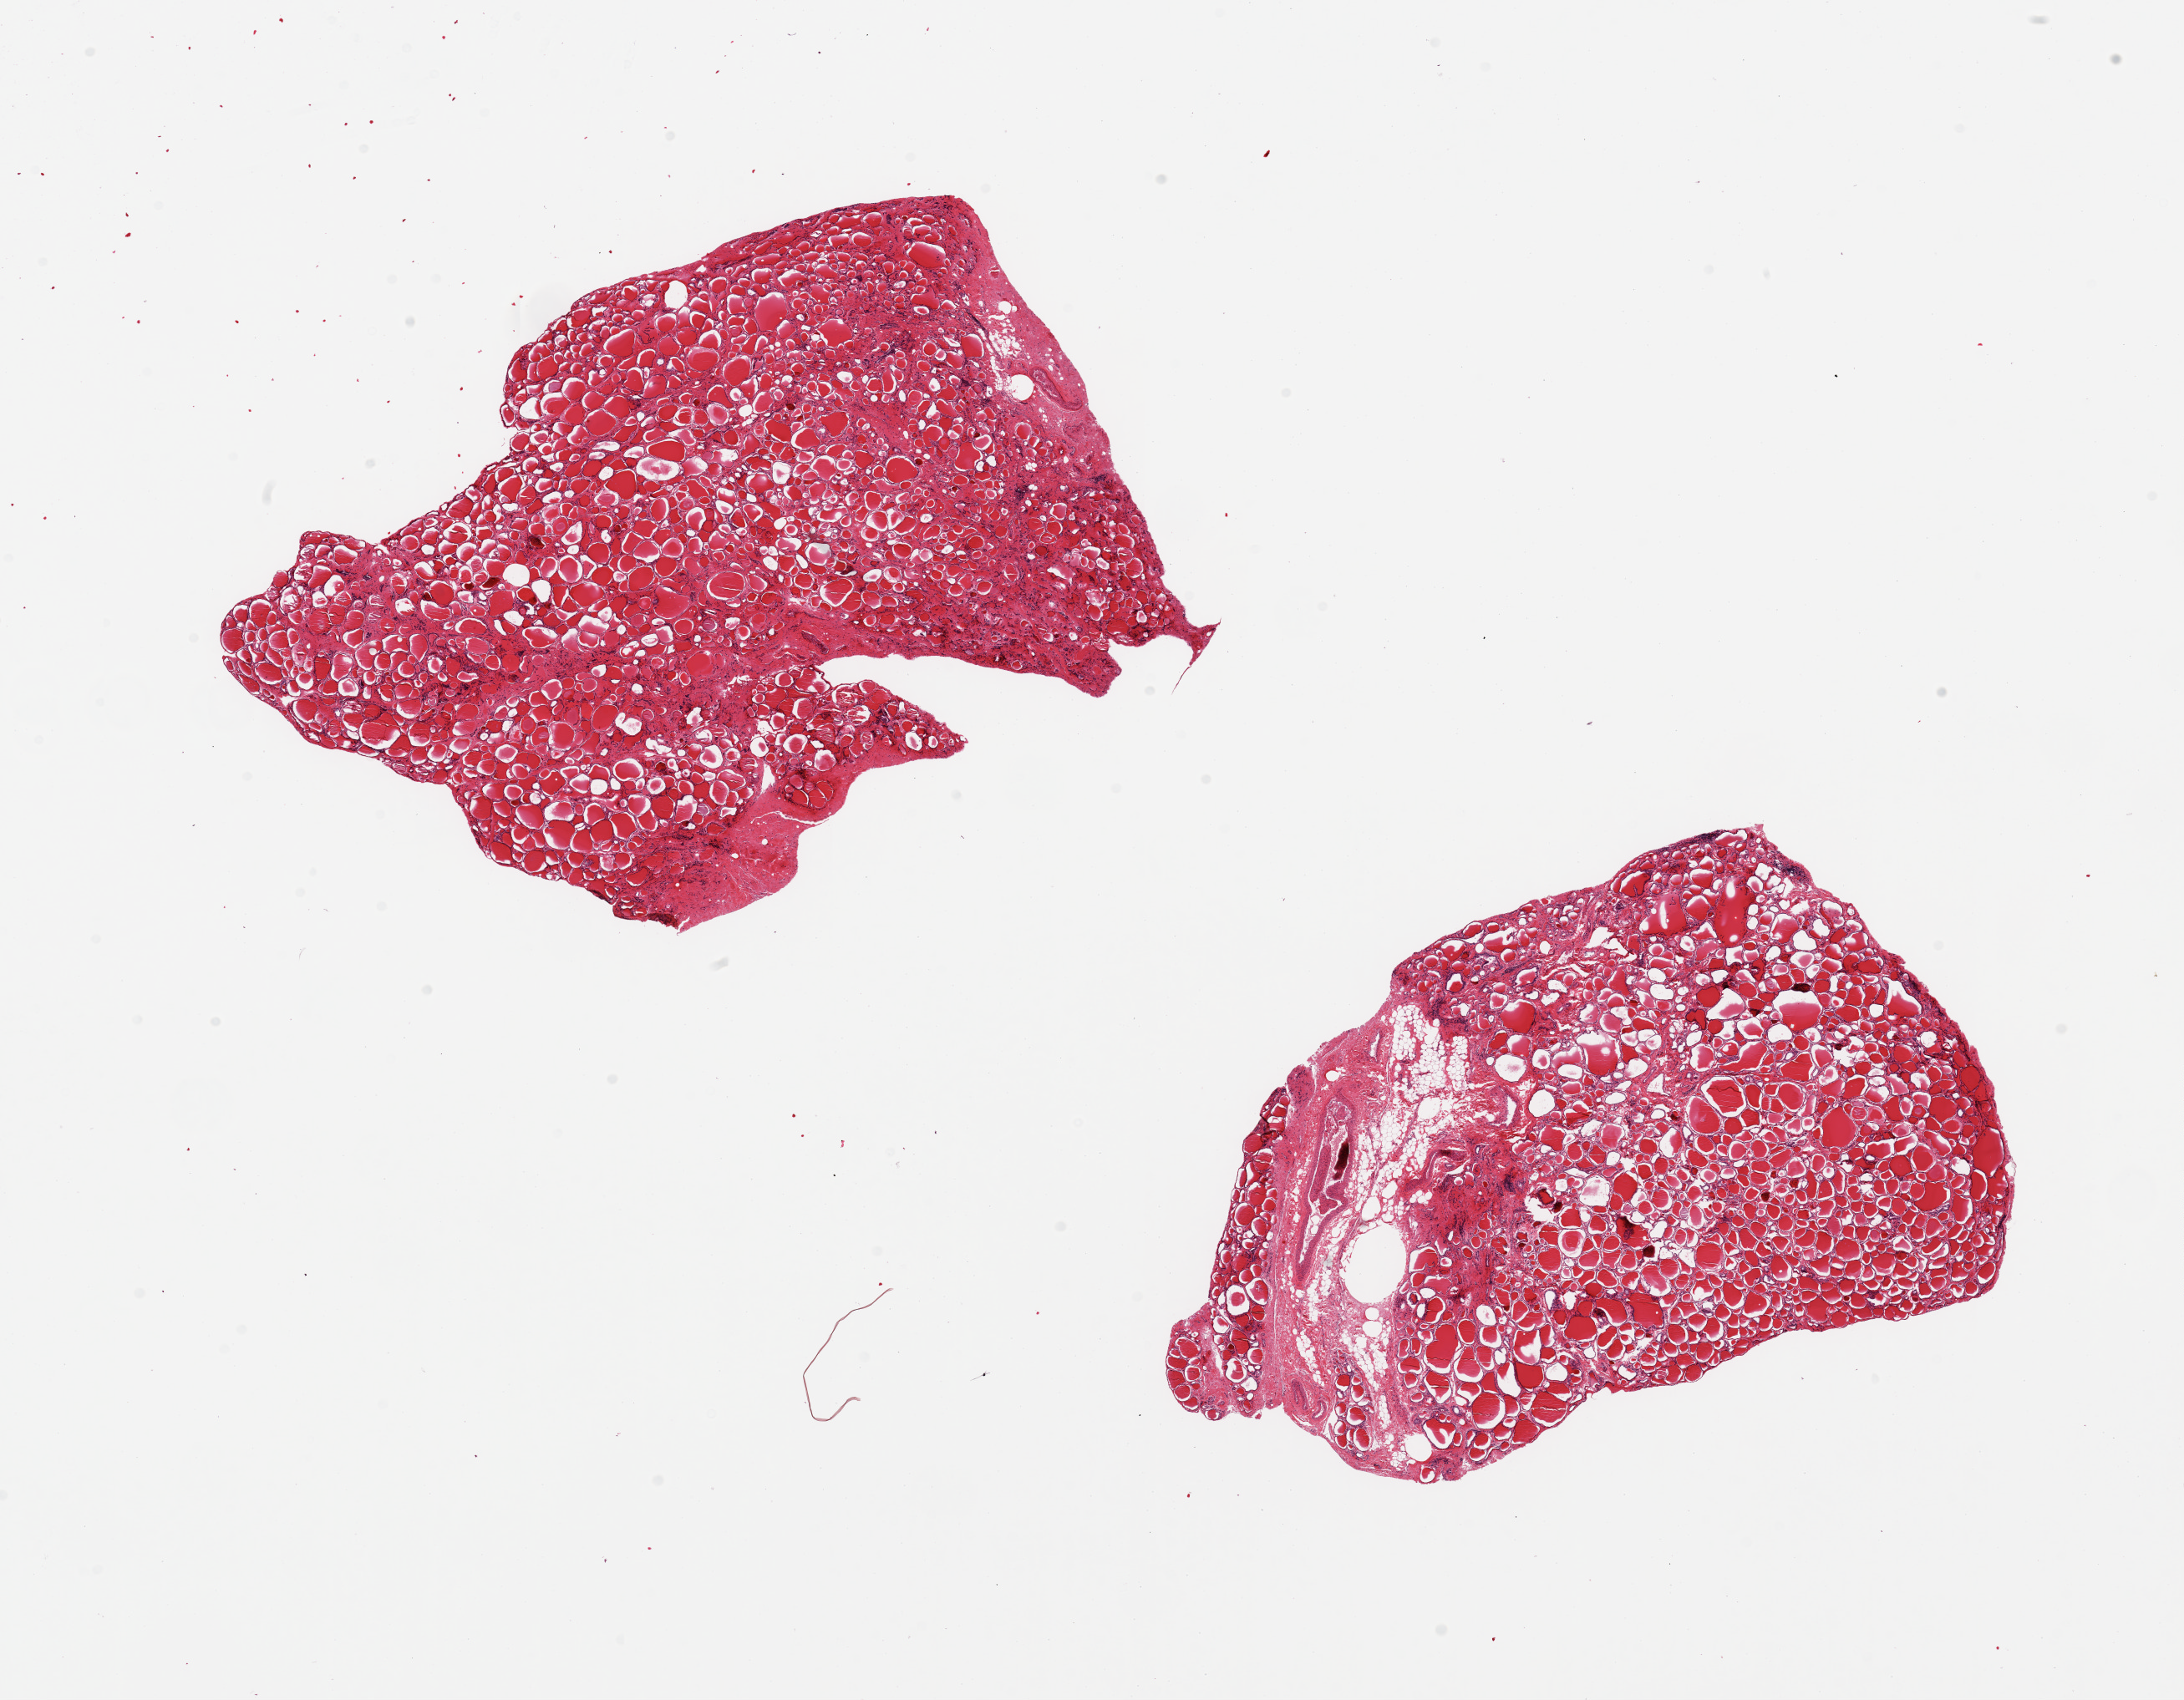
Hematoxylin and eosin (H&E) whole-slide image — a low-resolution overview of the entire scanned area, about 20.7 x 16.1 mm; PAXgene-fixed paraffin-embedded (PFPE) section; target tissue: thyroid; donor tissue sample. Male donor.
Reviewer comment on this tissue sample: 2 pieces; one piece is up to 20% fat/vessels.